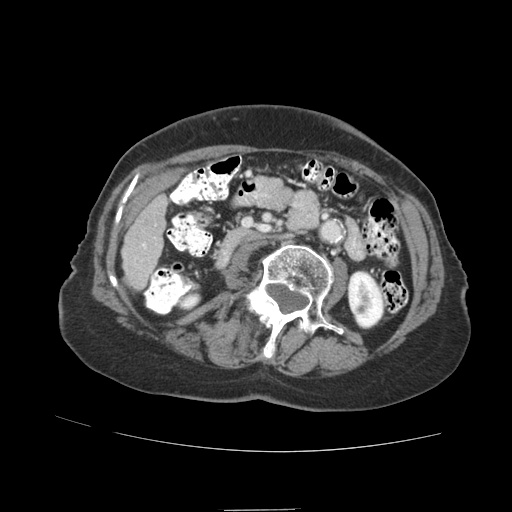
Contrast-enhanced abdominal CT (liver protocol), one axial slice; position 18 of 89 along the scan axis; reconstruction kernel STANDARD; 140 kVp; soft-tissue window (W 400 / L 40 HU); 2.5 mm slice thickness; 512 × 512 image matrix. Case-level facts recorded for this patient, not image findings: diagnosis: hepatocellular carcinoma (patient treated with transarterial chemoembolisation; whether this scan precedes or follows treatment is not stated here); TNM stage (as recorded): Stage-II; Child-Pugh class: A.
Annotated regions visible in this slice (semi-automatically segmented with operator editing):
- liver parenchyma outside the tumour (the mass and vessels are separate outlines, so this box may not span the whole liver): bounding box [x1, y1, x2, y2] px = [122, 176, 173, 290]
- liver vessels: [143, 243, 146, 248]